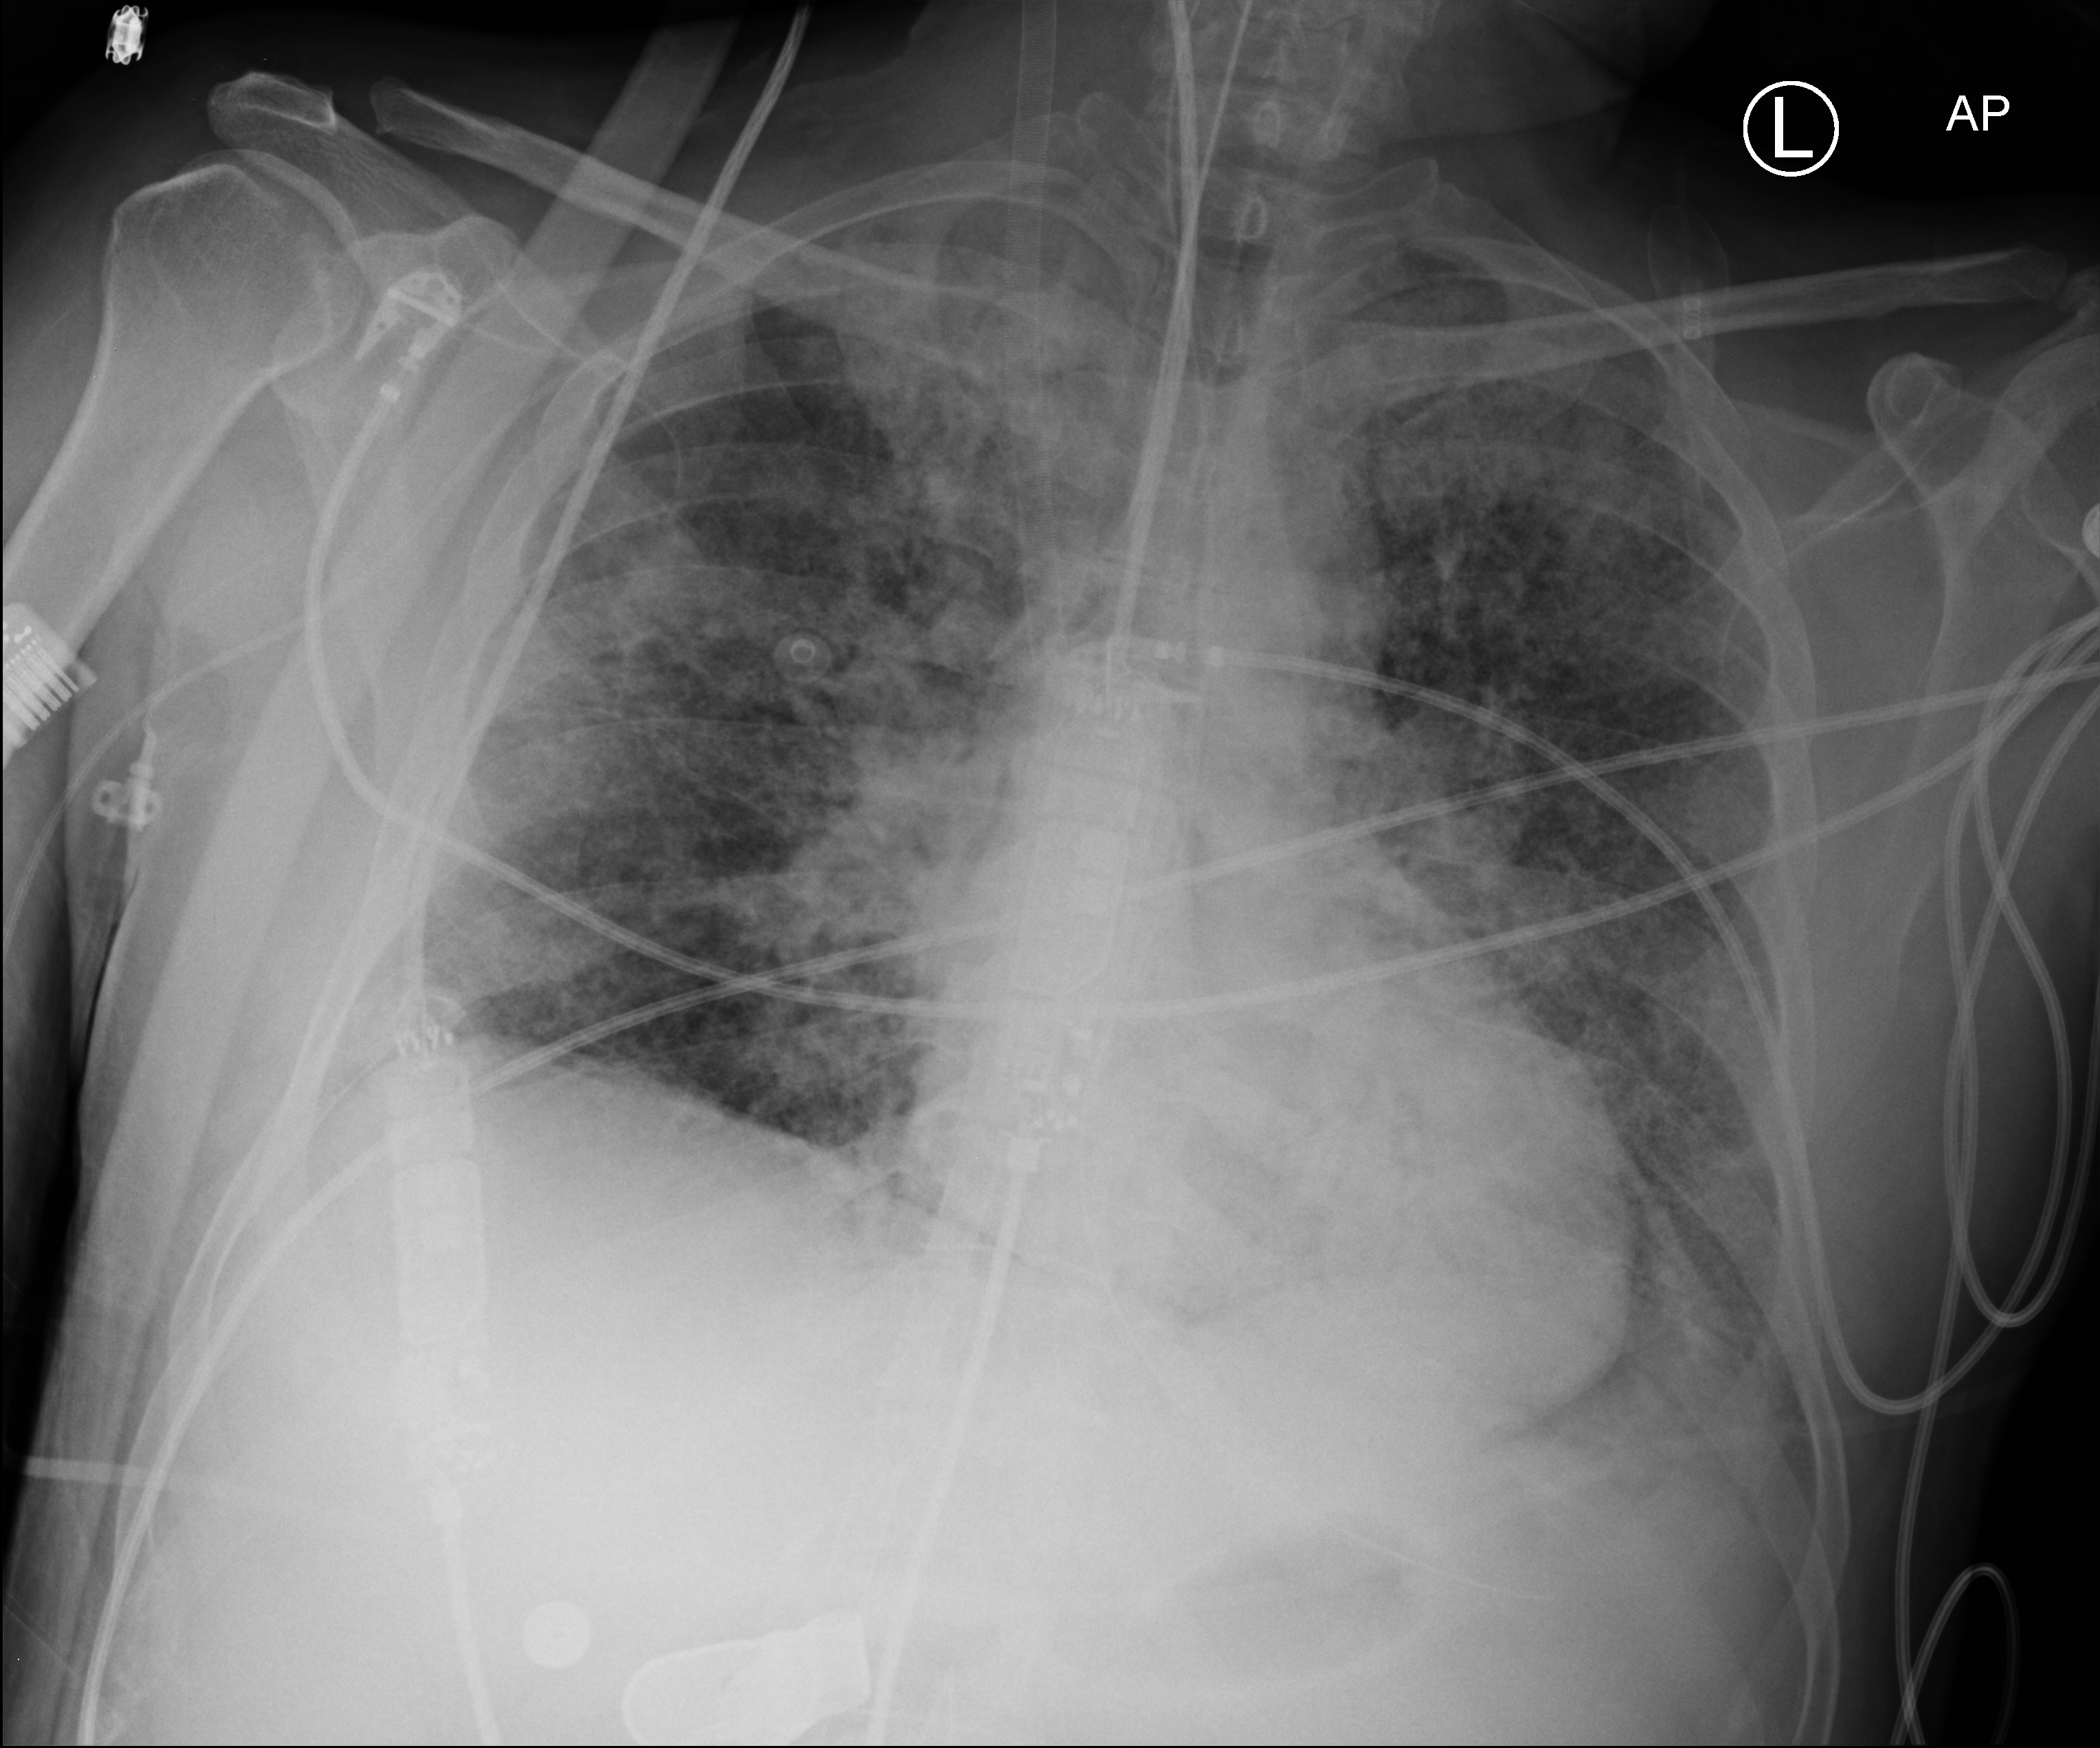
Bedside chest radiograph (computed radiography); anteroposterior (AP) projection. Male patient hospitalised with COVID-19, age 18–59 years.
From the hospital-stay record, not from the radiograph (when in the stay this image was taken is not recorded): length of hospital stay: 42 days.